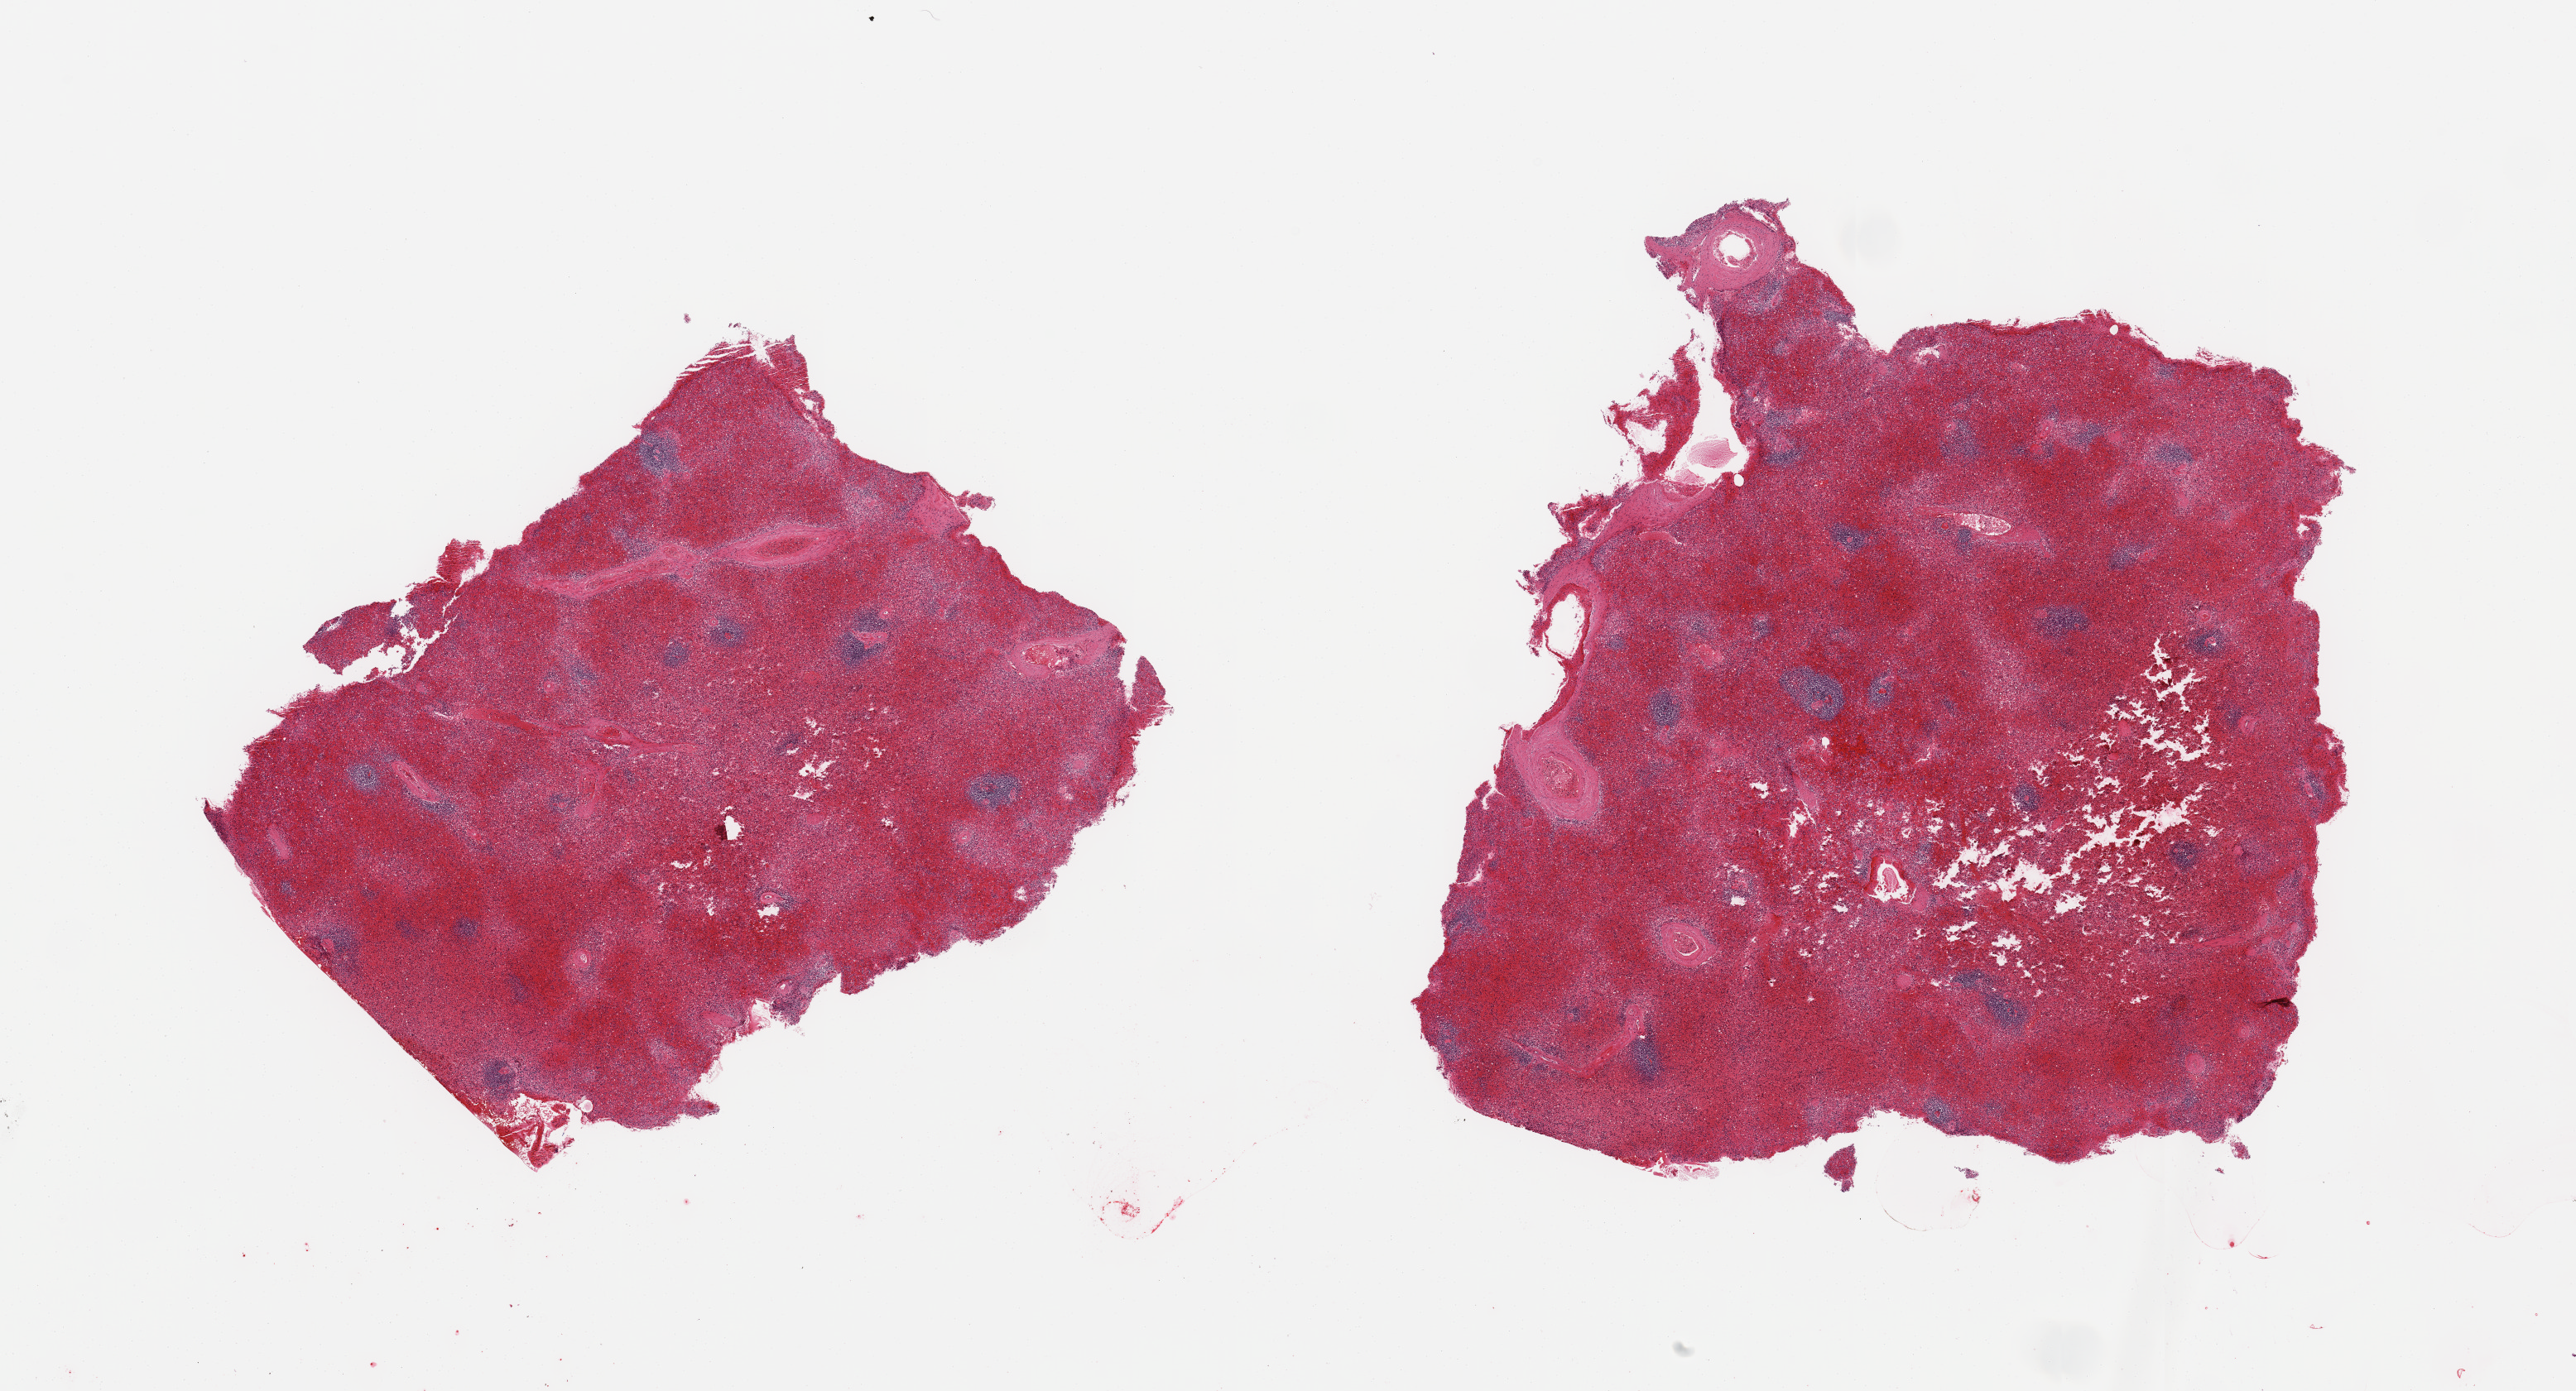
Digitized hematoxylin and eosin (H&E)-stained section, whole scanned area (about 24.6 x 13.3 mm, from a 20x scan) shown as a low-resolution overview, PAXgene-fixed, paraffin-embedded tissue, sampled site (target tissue): spleen, tissue donor sample. Male donor.
Review note (as recorded): 2 pieces; congested.